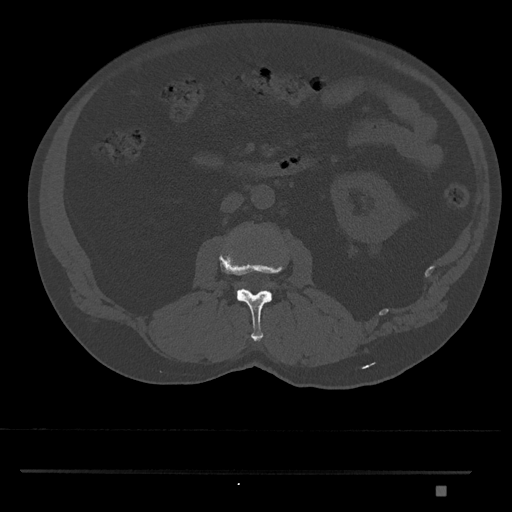
CT including the spine, one axial slice. Slice 732 of 1134 in the series (ordered by position). 120 kVp. Bone window (W 1800 / L 400 HU). 0.5 mm slice thickness. 512 × 512 image matrix, field of view 429 × 429 mm. Patient: male, 65 years. From the clinical record (not read from this slice): primary cancer: prostate.
Outlined on this slice (semi-automatically segmented with operator editing):
- L2 vertebra: bounding box <219,249,284,341> (left, top, right, bottom; pixels)